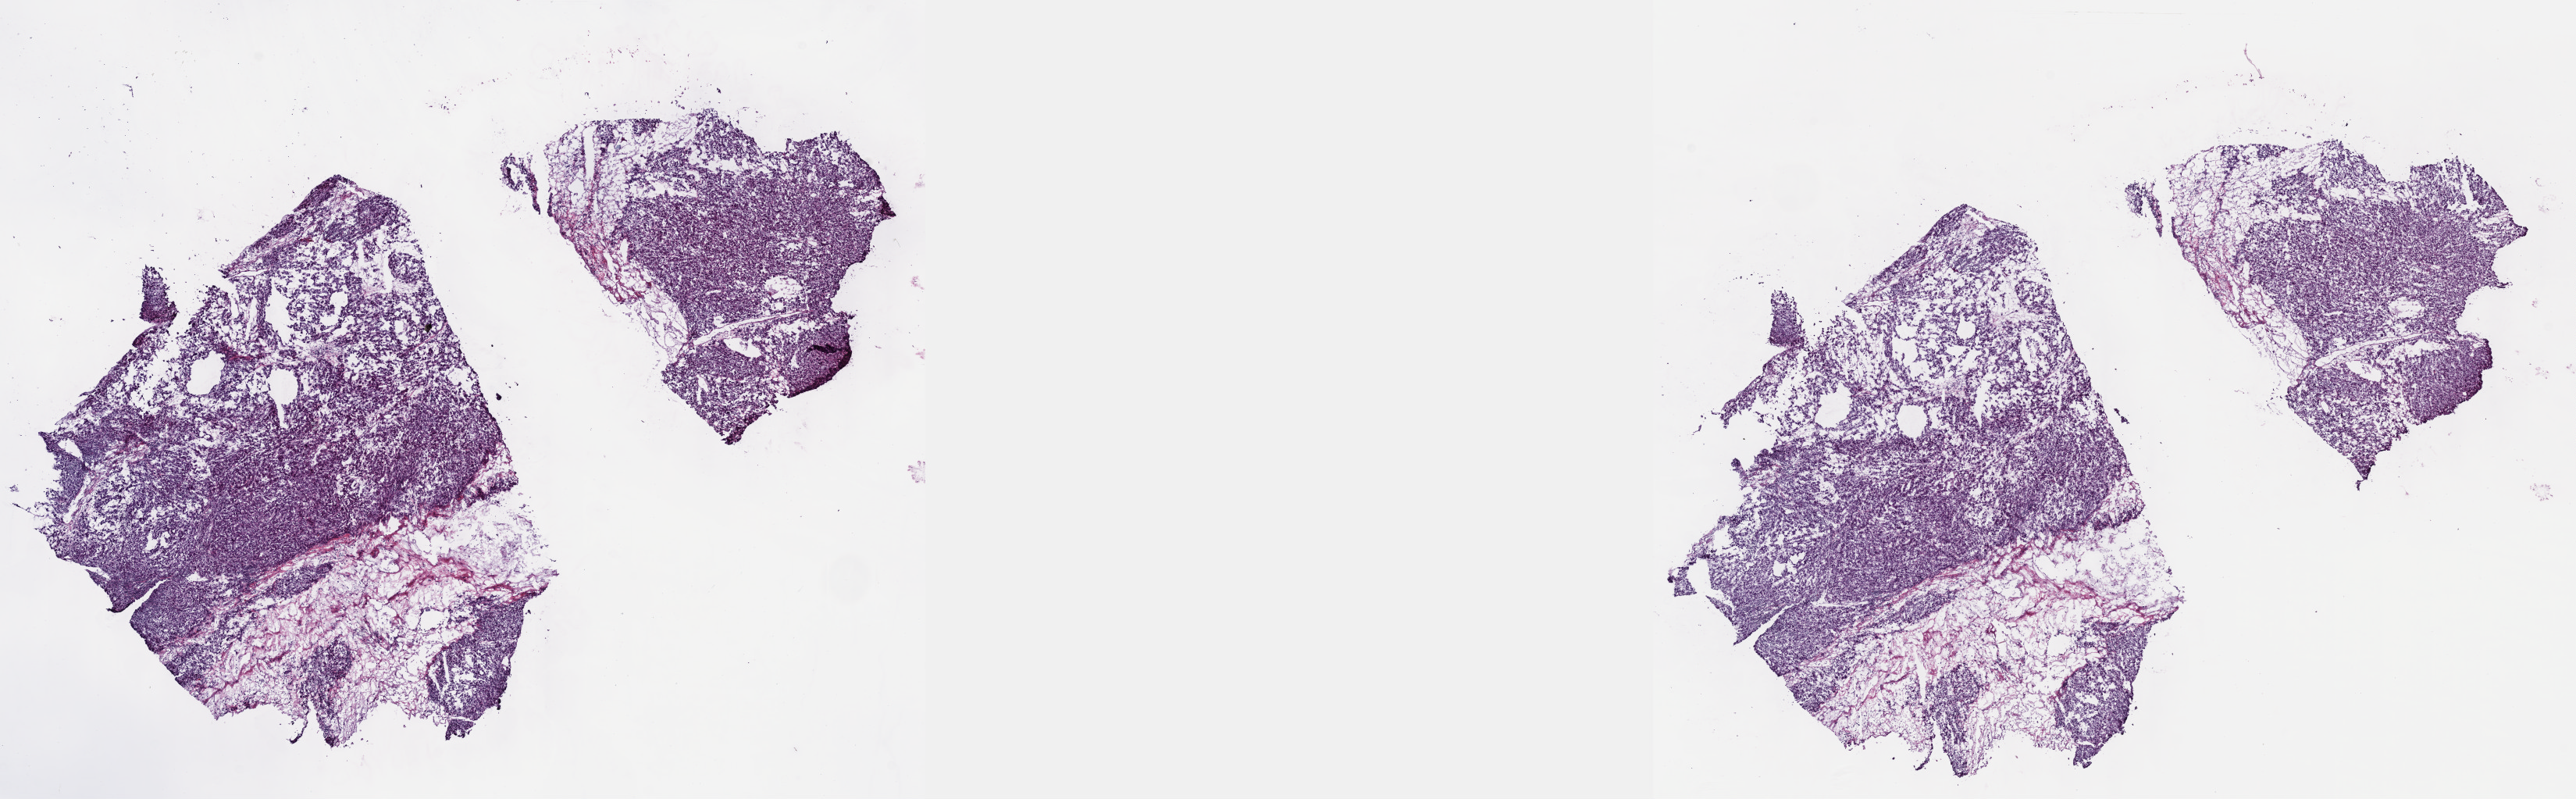
Hematoxylin and eosin (H&E) stained whole-slide image, a low-resolution overview of the entire scanned area, about 26.7 x 8.3 mm. Frozen section from the top of the tissue portion. Sample: primary tumour, liver. Patient: male, age at initial diagnosis 45 years. Histologic grade: G1 (well differentiated). Composition of this section per pathologist review: tumour cells 75%, tumour nuclei 75%, normal cells 0%, stromal cells 25%, necrosis 0%. Inflammatory infiltration, as recorded: lymphocyte infiltration 3%, monocyte infiltration 1%, neutrophil infiltration 3%.
Diagnosis: Hepatocellular carcinoma, NOS. AJCC pathologic stage: II.